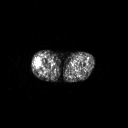
FDG PET of an extremity soft-tissue mass (from a PET/CT study), one axial slice; slice 229 of 267 in the series (ordered by position); 128 × 128 image matrix, field of view 700 × 700 mm. Male patient, age 43 years. Case-level facts recorded for this patient, not image findings: histological type: poorly differentiated synovial sarcoma; grade: high; site of the primary tumour: right buttock.
Structures marked on this image (expert contour drawn on MRI and transferred to this co-registered scan by the dataset authors):
- gross tumour volume including surrounding oedema: bounding box (x1, y1, x2, y2) in pixels: (34, 59, 43, 69)
- gross tumour volume (mass): (34, 59, 39, 68)